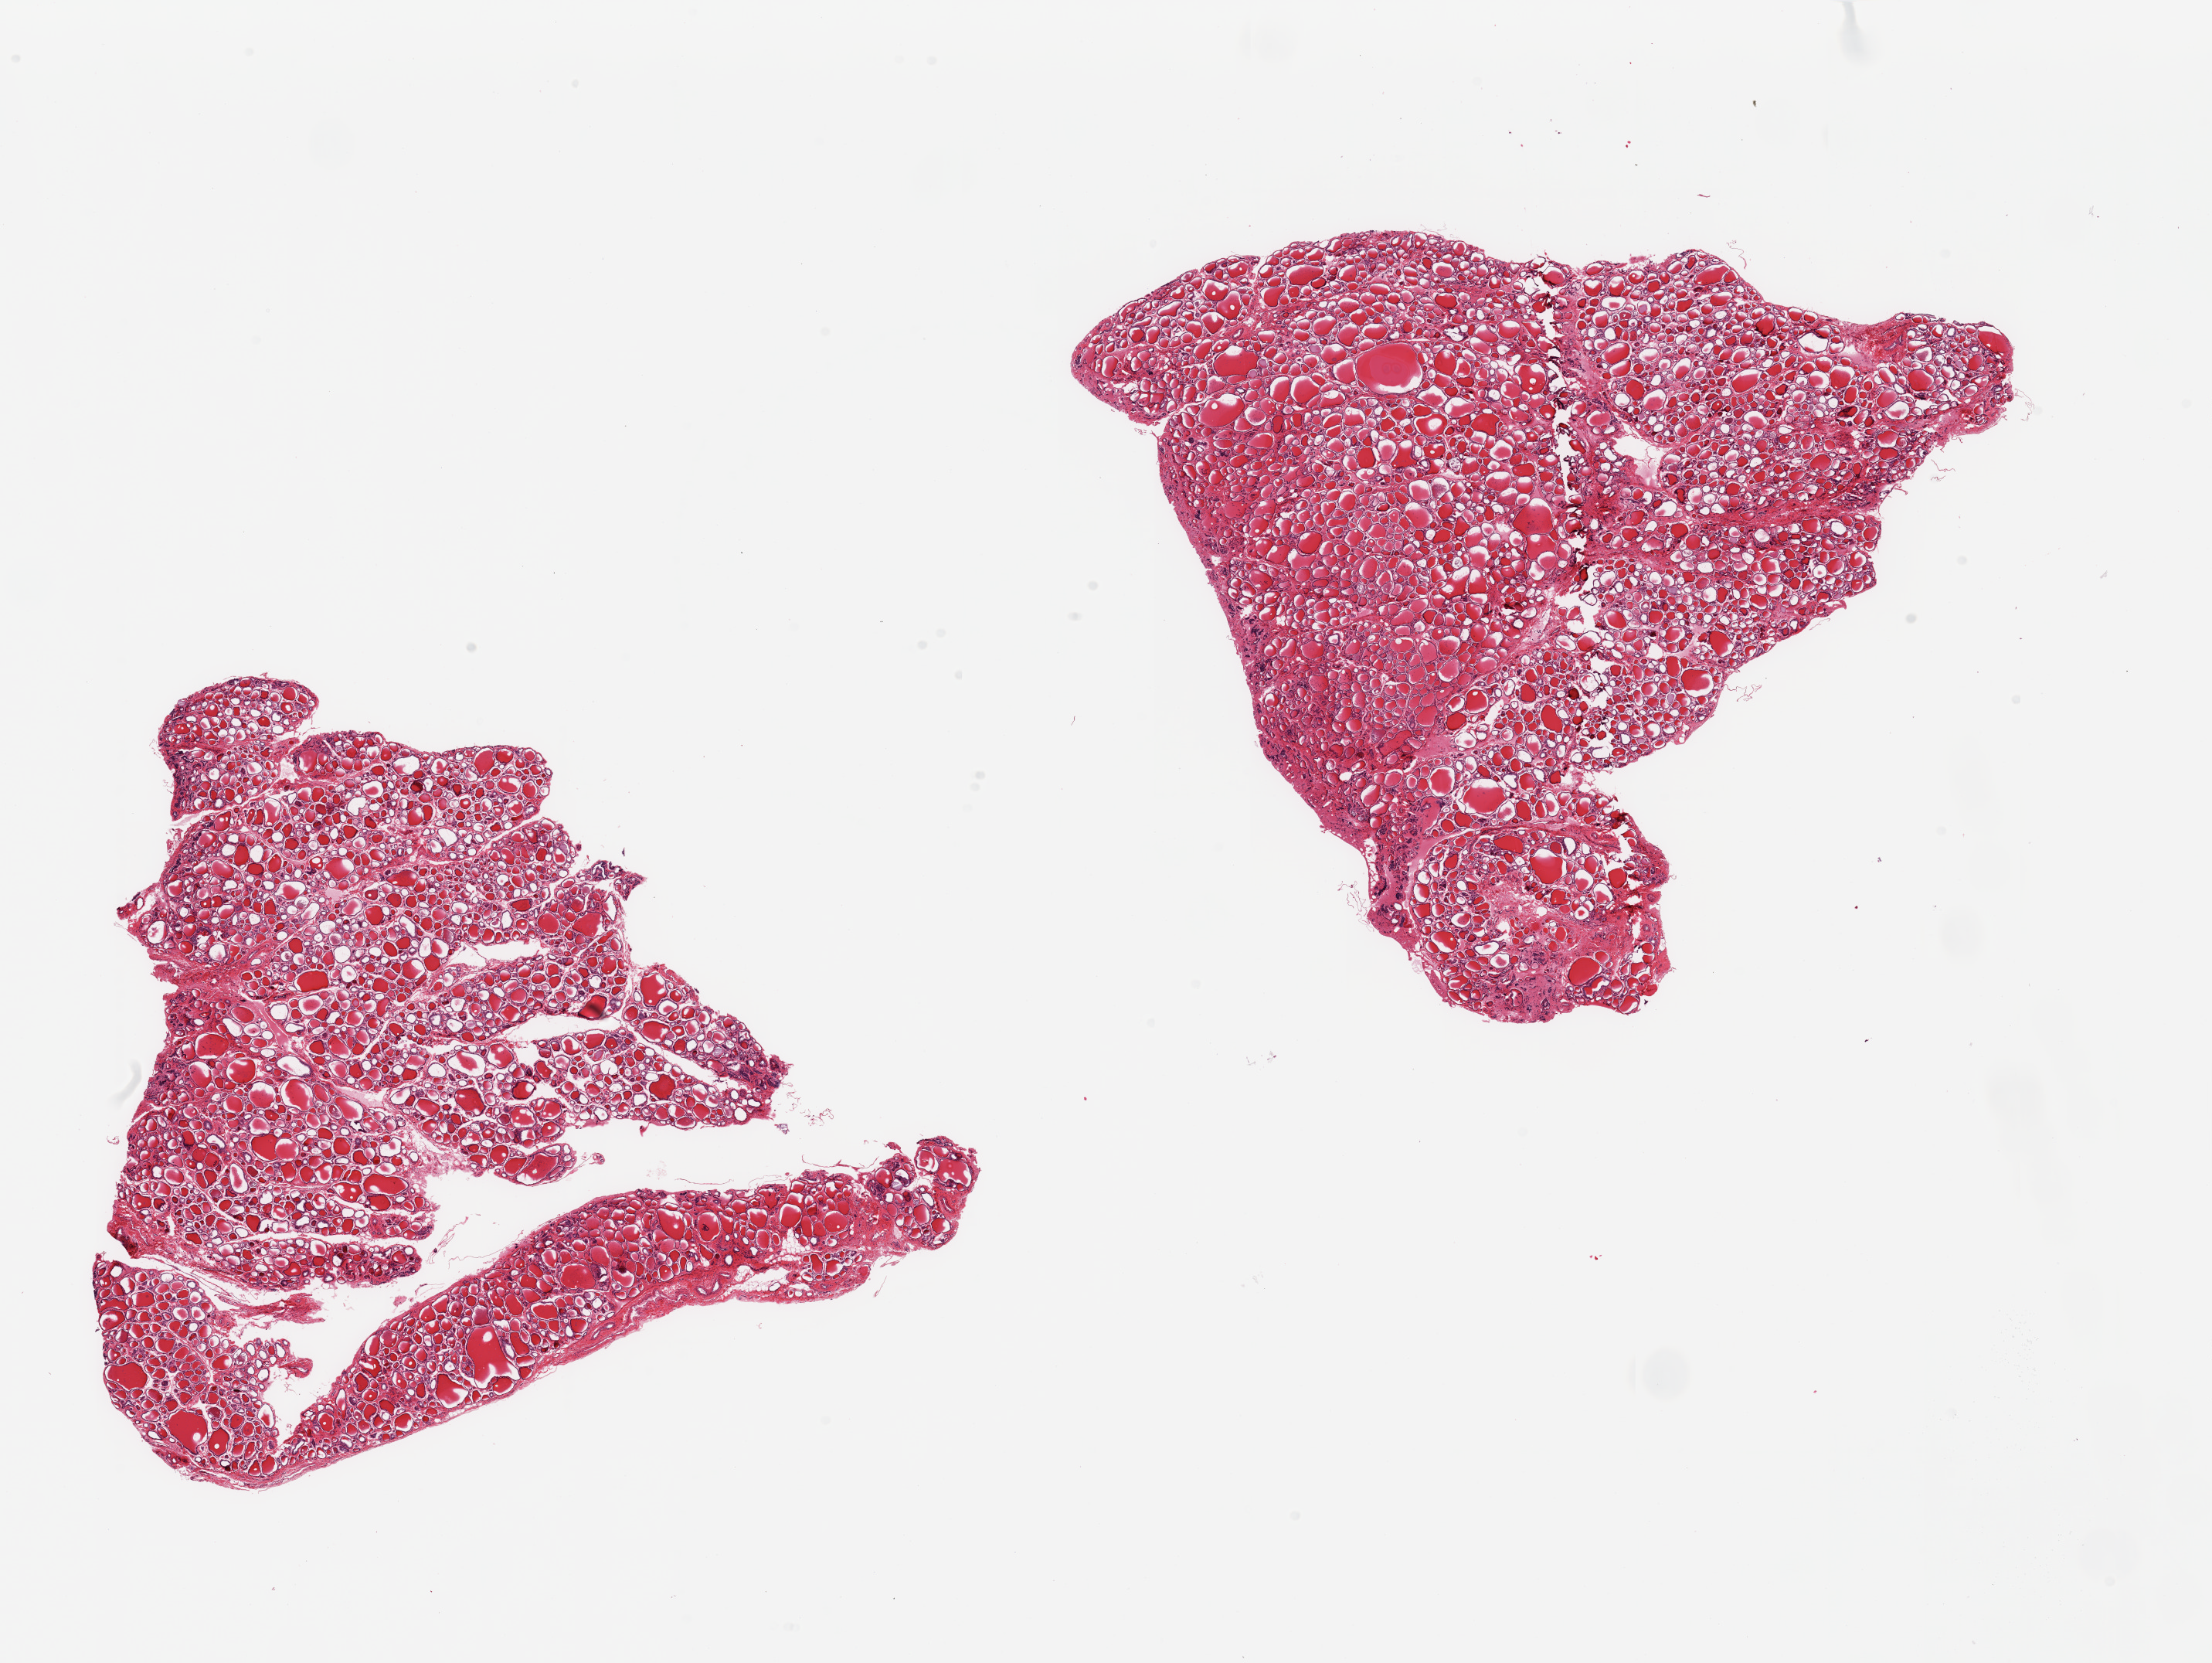
Haematoxylin and eosin whole-slide image — whole scanned area (about 22.6 x 17.0 mm, from a 20x scan) shown as a low-resolution overview. PAXgene-fixed paraffin-embedded (PFPE) section. Target tissue: thyroid. Donor tissue sample.
- review note (as recorded): 2 pieces, no abnormalities